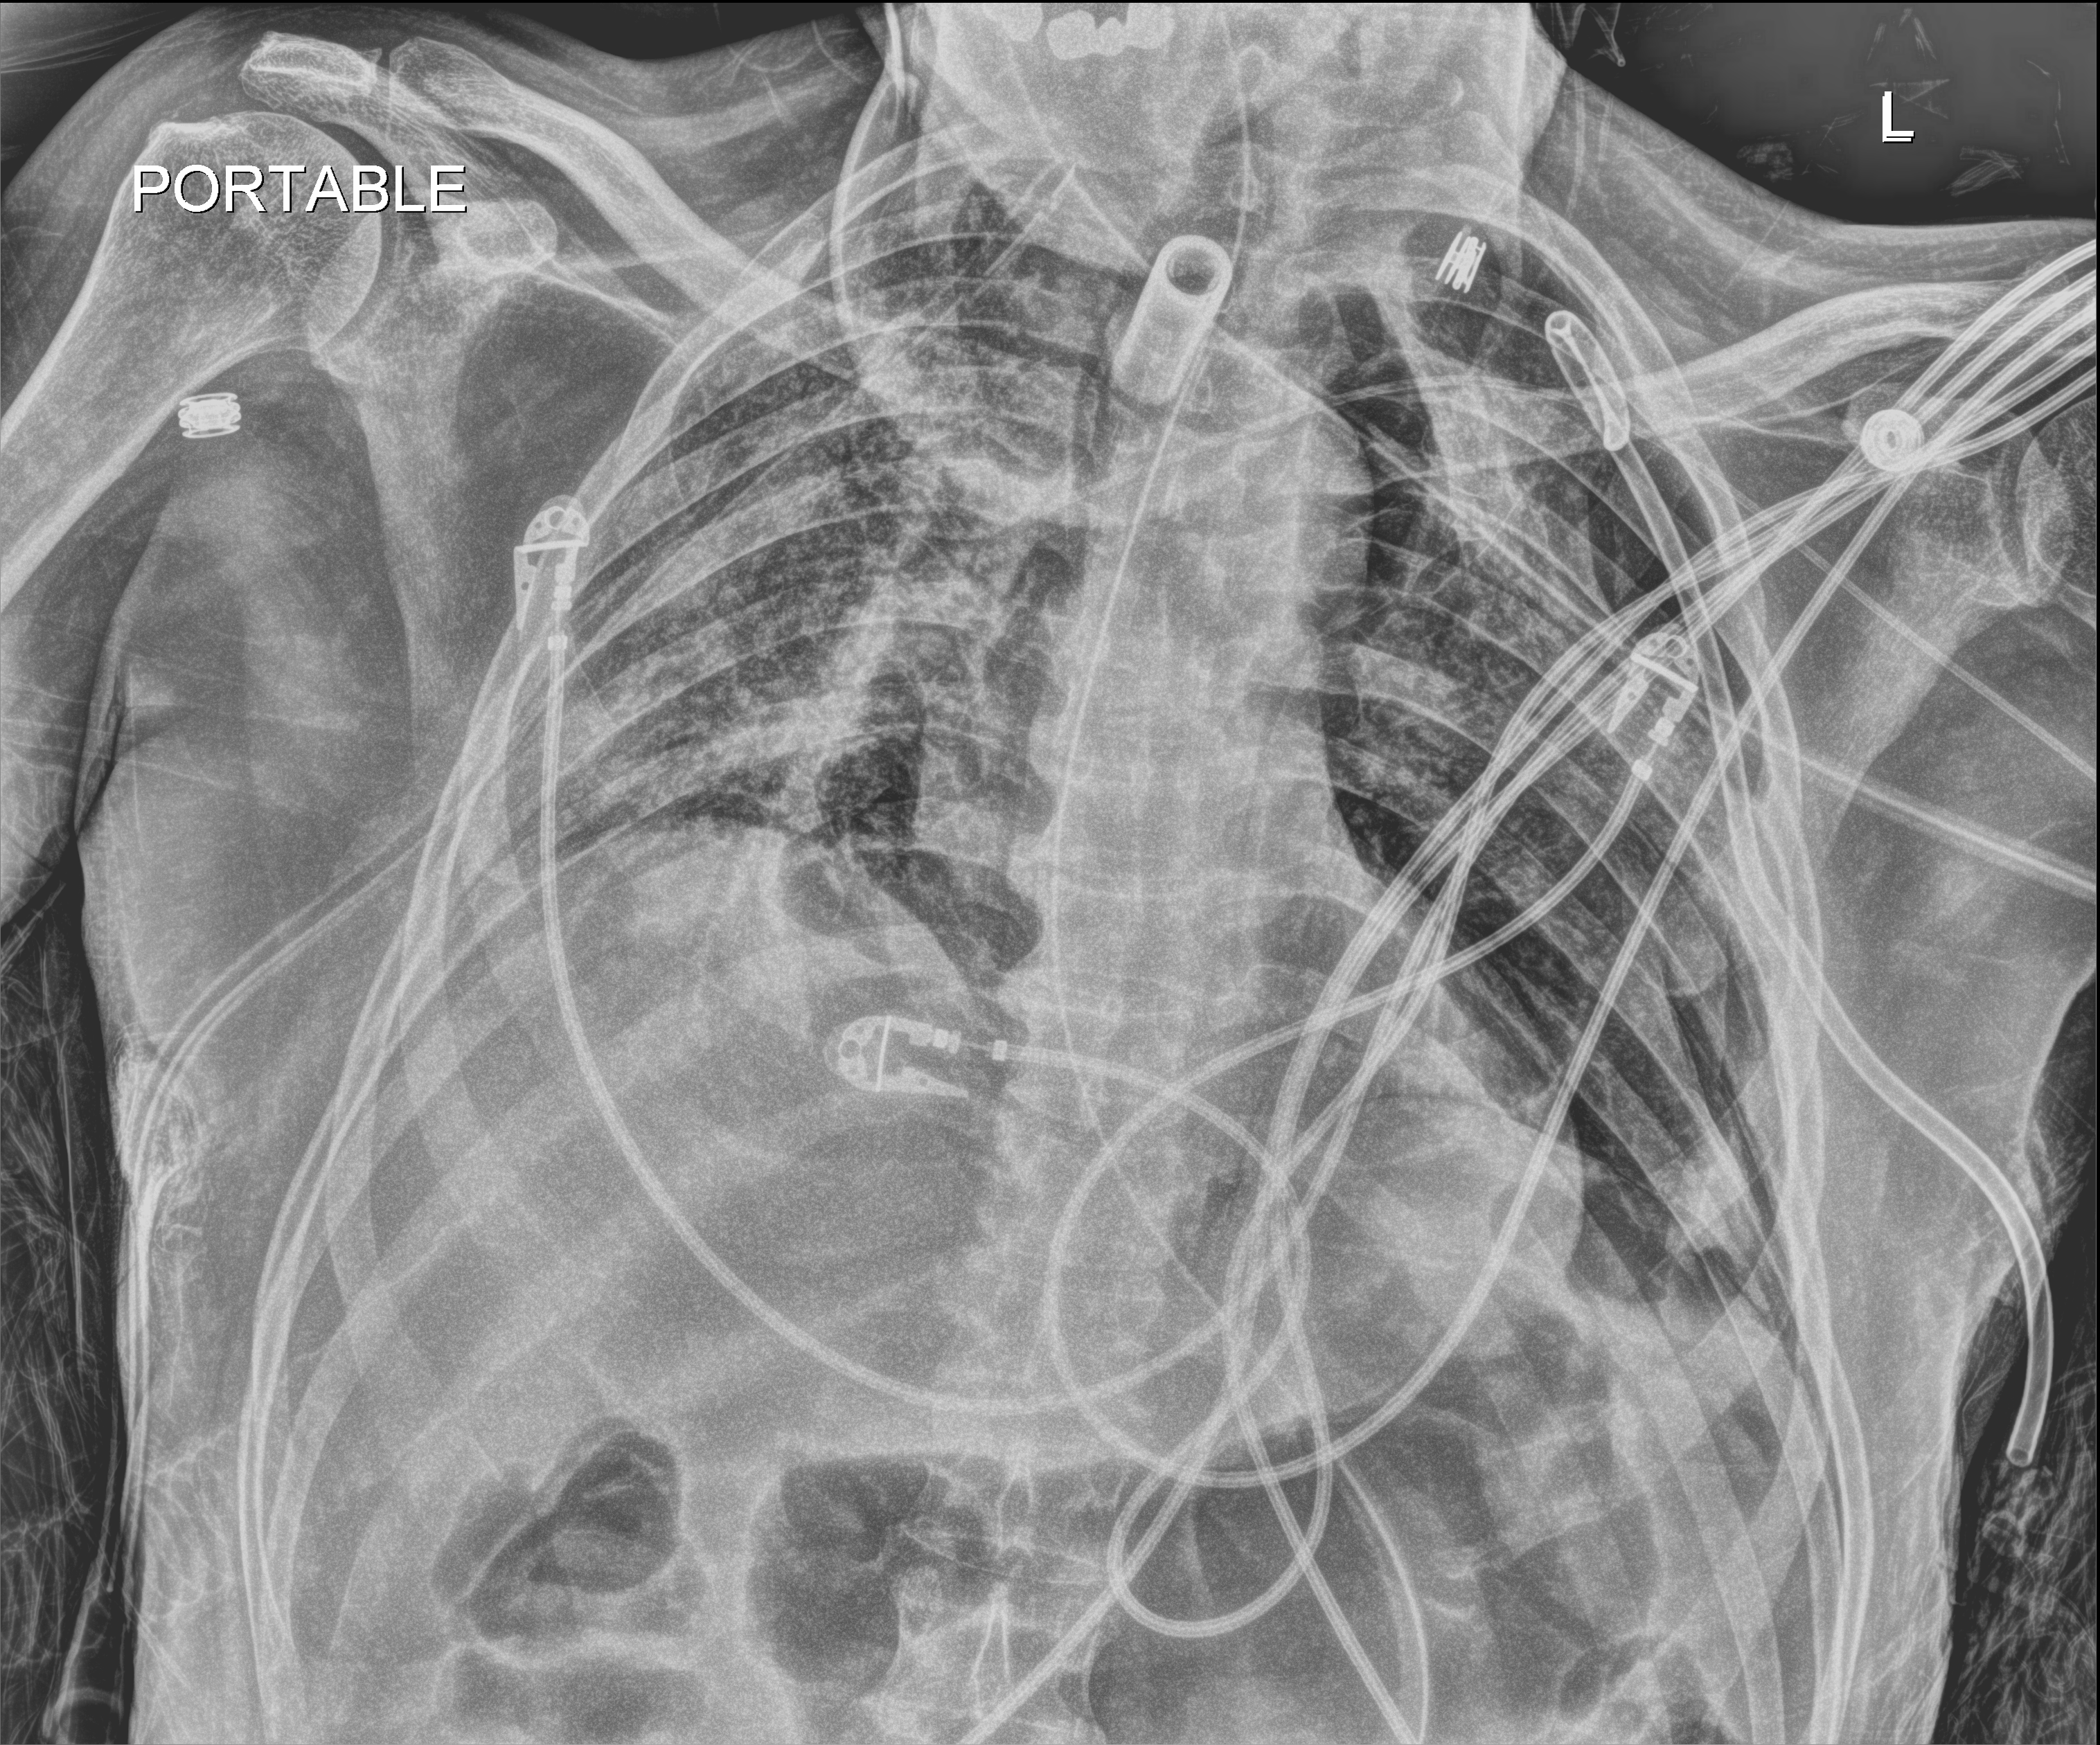
Portable chest radiograph; anteroposterior (AP) projection. Patient hospitalised with COVID-19; male, aged 18–59 years.
Hospital-stay facts (about this admission, not read from this image; timing relative to this image not recorded):
- admitted to intensive care during this hospital stay: yes